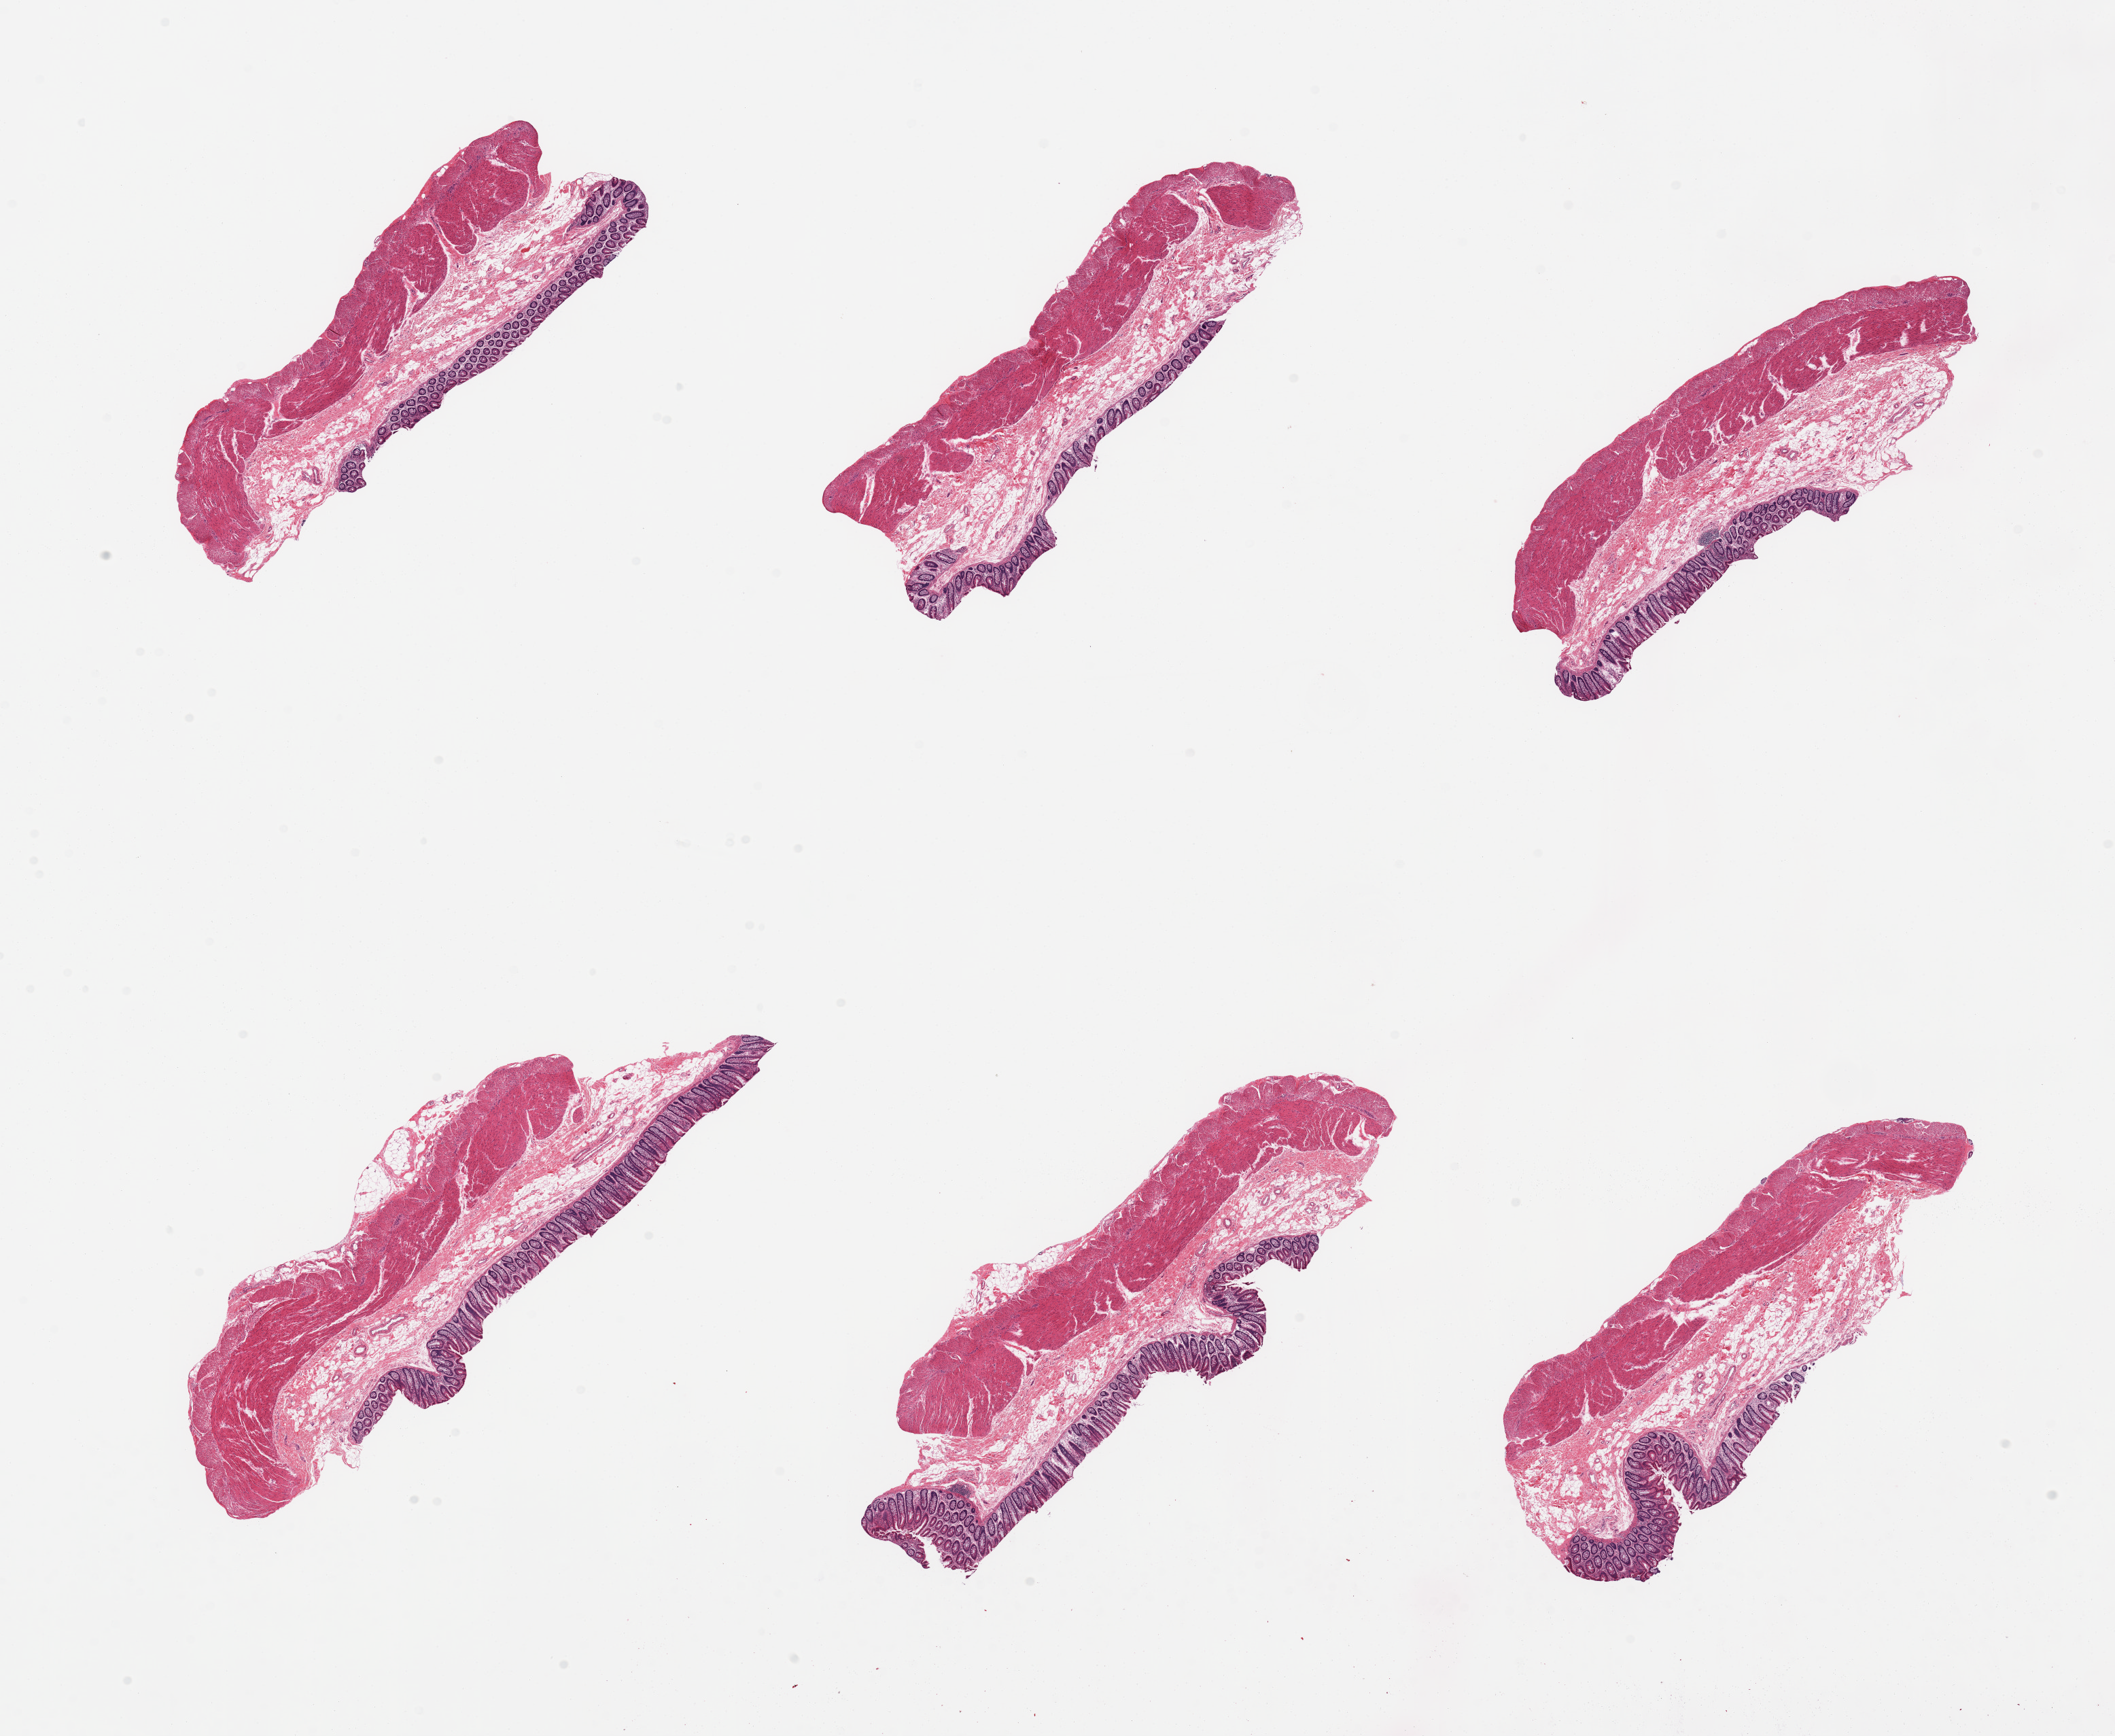
H&E whole-slide image, brightfield, a low-resolution overview of the entire scanned area, about 24.6 x 20.2 mm, PAXgene-fixed, paraffin-embedded tissue, target tissue: transverse colon, donor tissue sample. Donor sex: female.
Reviewer comment on this tissue sample: 6 pieces, mucosa well preserved, up to ~0.4mm thick.